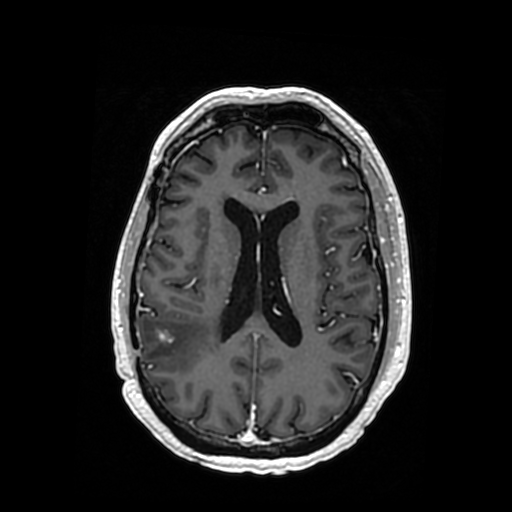
Brain MRI from a brain-tumour surgery series, one axial slice. Slice 153 of 364 in the series (ordered by position). T1-weighted post-contrast. 512 × 512 image matrix, field of view 260 × 260 mm. From the clinical record (not read from this slice): histopathology: Oligodendroglioma; WHO grade: 3; IDH mutation: yes; tumour location: Right Posterior Temporal Inferior Parietal.
Annotated regions visible in this slice (manually delineated by an expert):
- tumour: box from (x=172, y=327) to (x=189, y=343) px